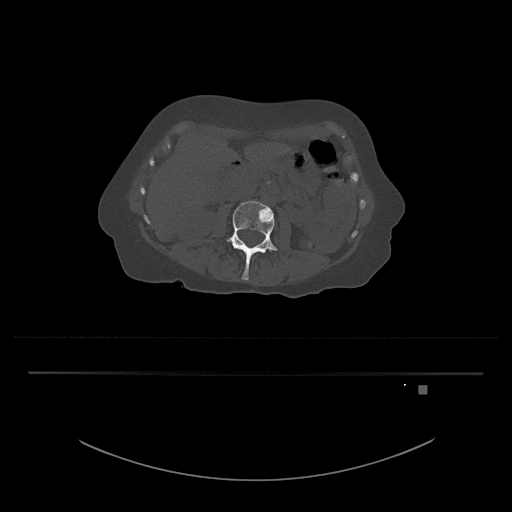
CT including the spine, one axial slice. Position 428 of 797 along the scan axis. Reconstruction kernel Br40s/3. Bone window (W 1800 / L 400 HU). 512 × 512 image matrix. Patient: female, 57 years. Case-level facts recorded for this patient, not image findings: primary cancer: cervical.
Structures marked on this image (semi-automatic segmentation, software-assisted and operator-edited):
- L3 vertebra: box from (x=225, y=201) to (x=278, y=281) px